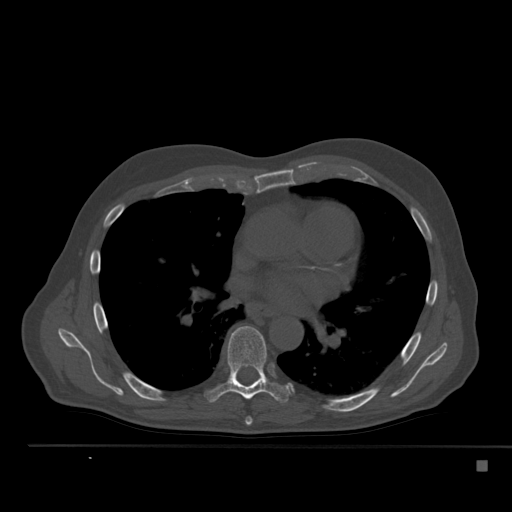
CT including the spine, one axial slice; slice 329 of 517 in the series (ordered by position); reconstruction kernel Br40s; 120 kVp; bone window (W 1800 / L 400 HU); 1.5 mm slice thickness; 512 × 512 image matrix, field of view 408 × 408 mm. Male patient, age 70 years. Case-level facts recorded for this patient, not image findings: primary cancer: renal; vertebrae with lytic lesions (as recorded): T4, T6, T10, T12, L3, L4, L5.
Structures marked on this image (semi-automatic segmentation, software-assisted and operator-edited):
- T6 vertebra: bounding box (x1, y1, x2, y2) in pixels: (245, 417, 253, 425)
- T7 vertebra: (206, 326, 291, 403)